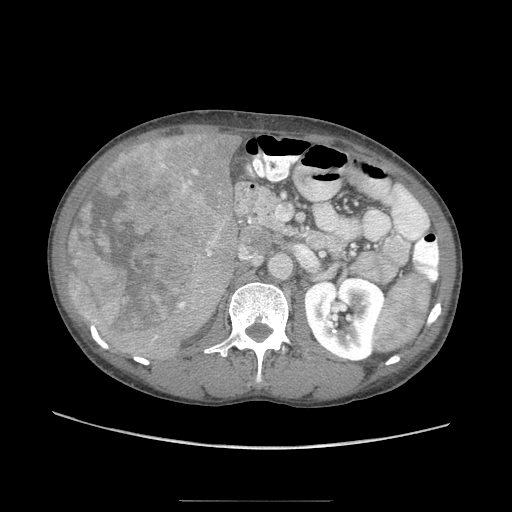
Contrast-enhanced abdominal CT (liver protocol), one axial slice. Reconstruction kernel STANDARD. Soft-tissue window (W 400 / L 40 HU). 2.5 mm slice thickness. 512 × 512 image matrix, field of view 380 × 380 mm. From the clinical record (not read from this slice): diagnosis: hepatocellular carcinoma (patient treated with transarterial chemoembolisation; whether this scan precedes or follows treatment is not stated here); TNM stage (as recorded): Stage-IIIA; Child-Pugh class: A; tumour size: 16 cm.
Structures marked on this image (semi-automatic segmentation, software-assisted and operator-edited):
- liver parenchyma outside the tumour (the mass and vessels are separate outlines, so this box may not span the whole liver): box from (x=70, y=130) to (x=242, y=354) px
- mass: (x=65, y=140)–(x=220, y=345)
- liver vessels: (x=197, y=262)–(x=199, y=265)